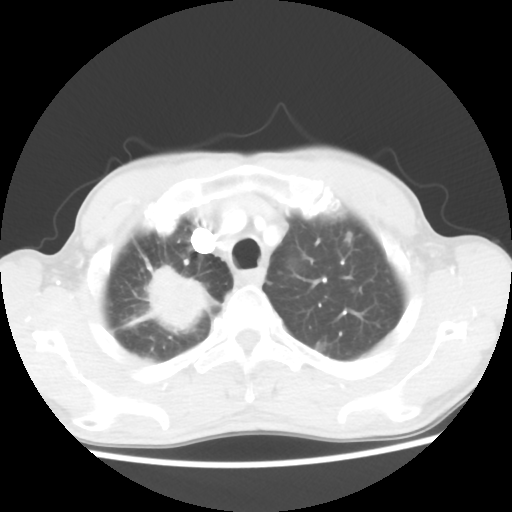
Chest CT, one axial slice; slice 44 of 52 in the series (ordered by position); 100 kVp; lung window (W 1500 / L -600 HU); 512 × 512 image matrix. Male patient, age 66 years. From the clinical record (not read from this slice): clinical TNM (as recorded): T2 N0 M1a.
Annotated regions visible in this slice (bounding box drawn by a radiologist):
- lung tumour (recorded histology: adenocarcinoma): bounding box [x1, y1, x2, y2] px = [131, 260, 217, 334]